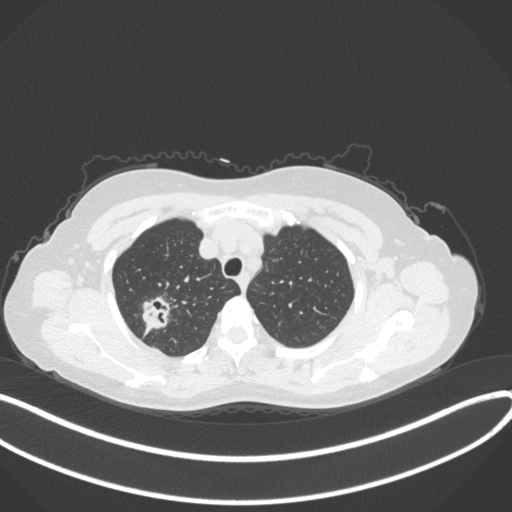
Chest CT, one axial slice. Slice 298 of 342 in the series (ordered by position). Lung window (W 1500 / L -600 HU). 1 mm slice thickness. 512 × 512 image matrix, field of view 400 × 400 mm. Female patient, age 50 years. Case-level facts recorded for this patient, not image findings: clinical TNM (as recorded): T1c N0 M0; histopathological grade: G2-3.
Structures marked on this image (bounding box drawn by a radiologist):
- lung tumour (recorded histology: adenocarcinoma): box from (x=137, y=291) to (x=175, y=333) px